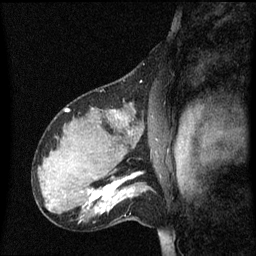
Breast MRI (dynamic contrast-enhanced), one sagittal slice. Slice 41 of 60 in the series (ordered by position). Dynamic contrast-enhanced series, image 2 of 3 at this slice position (ordered by acquisition). 1.5 T. TE 4.2 ms, TR 8.4 ms. 256 × 256 image matrix, field of view 210 × 210 mm. Female patient, age 31 years. Case-level facts recorded for this patient, not image findings: setting: breast cancer imaged before/during neoadjuvant chemotherapy; receptor status: HR-positive, HER2-negative.
Annotated regions visible in this slice (semi-automatically segmented with operator editing):
- analysis volume of interest (the breast-tissue region the enhancement analysis was run in; not a lesion): bounding box [x1, y1, x2, y2] px = [98, 175, 151, 224]
- tumour enhancement mask (voxels above the 70 % enhancement threshold inside the analysis volume of interest): [98, 175, 137, 211]